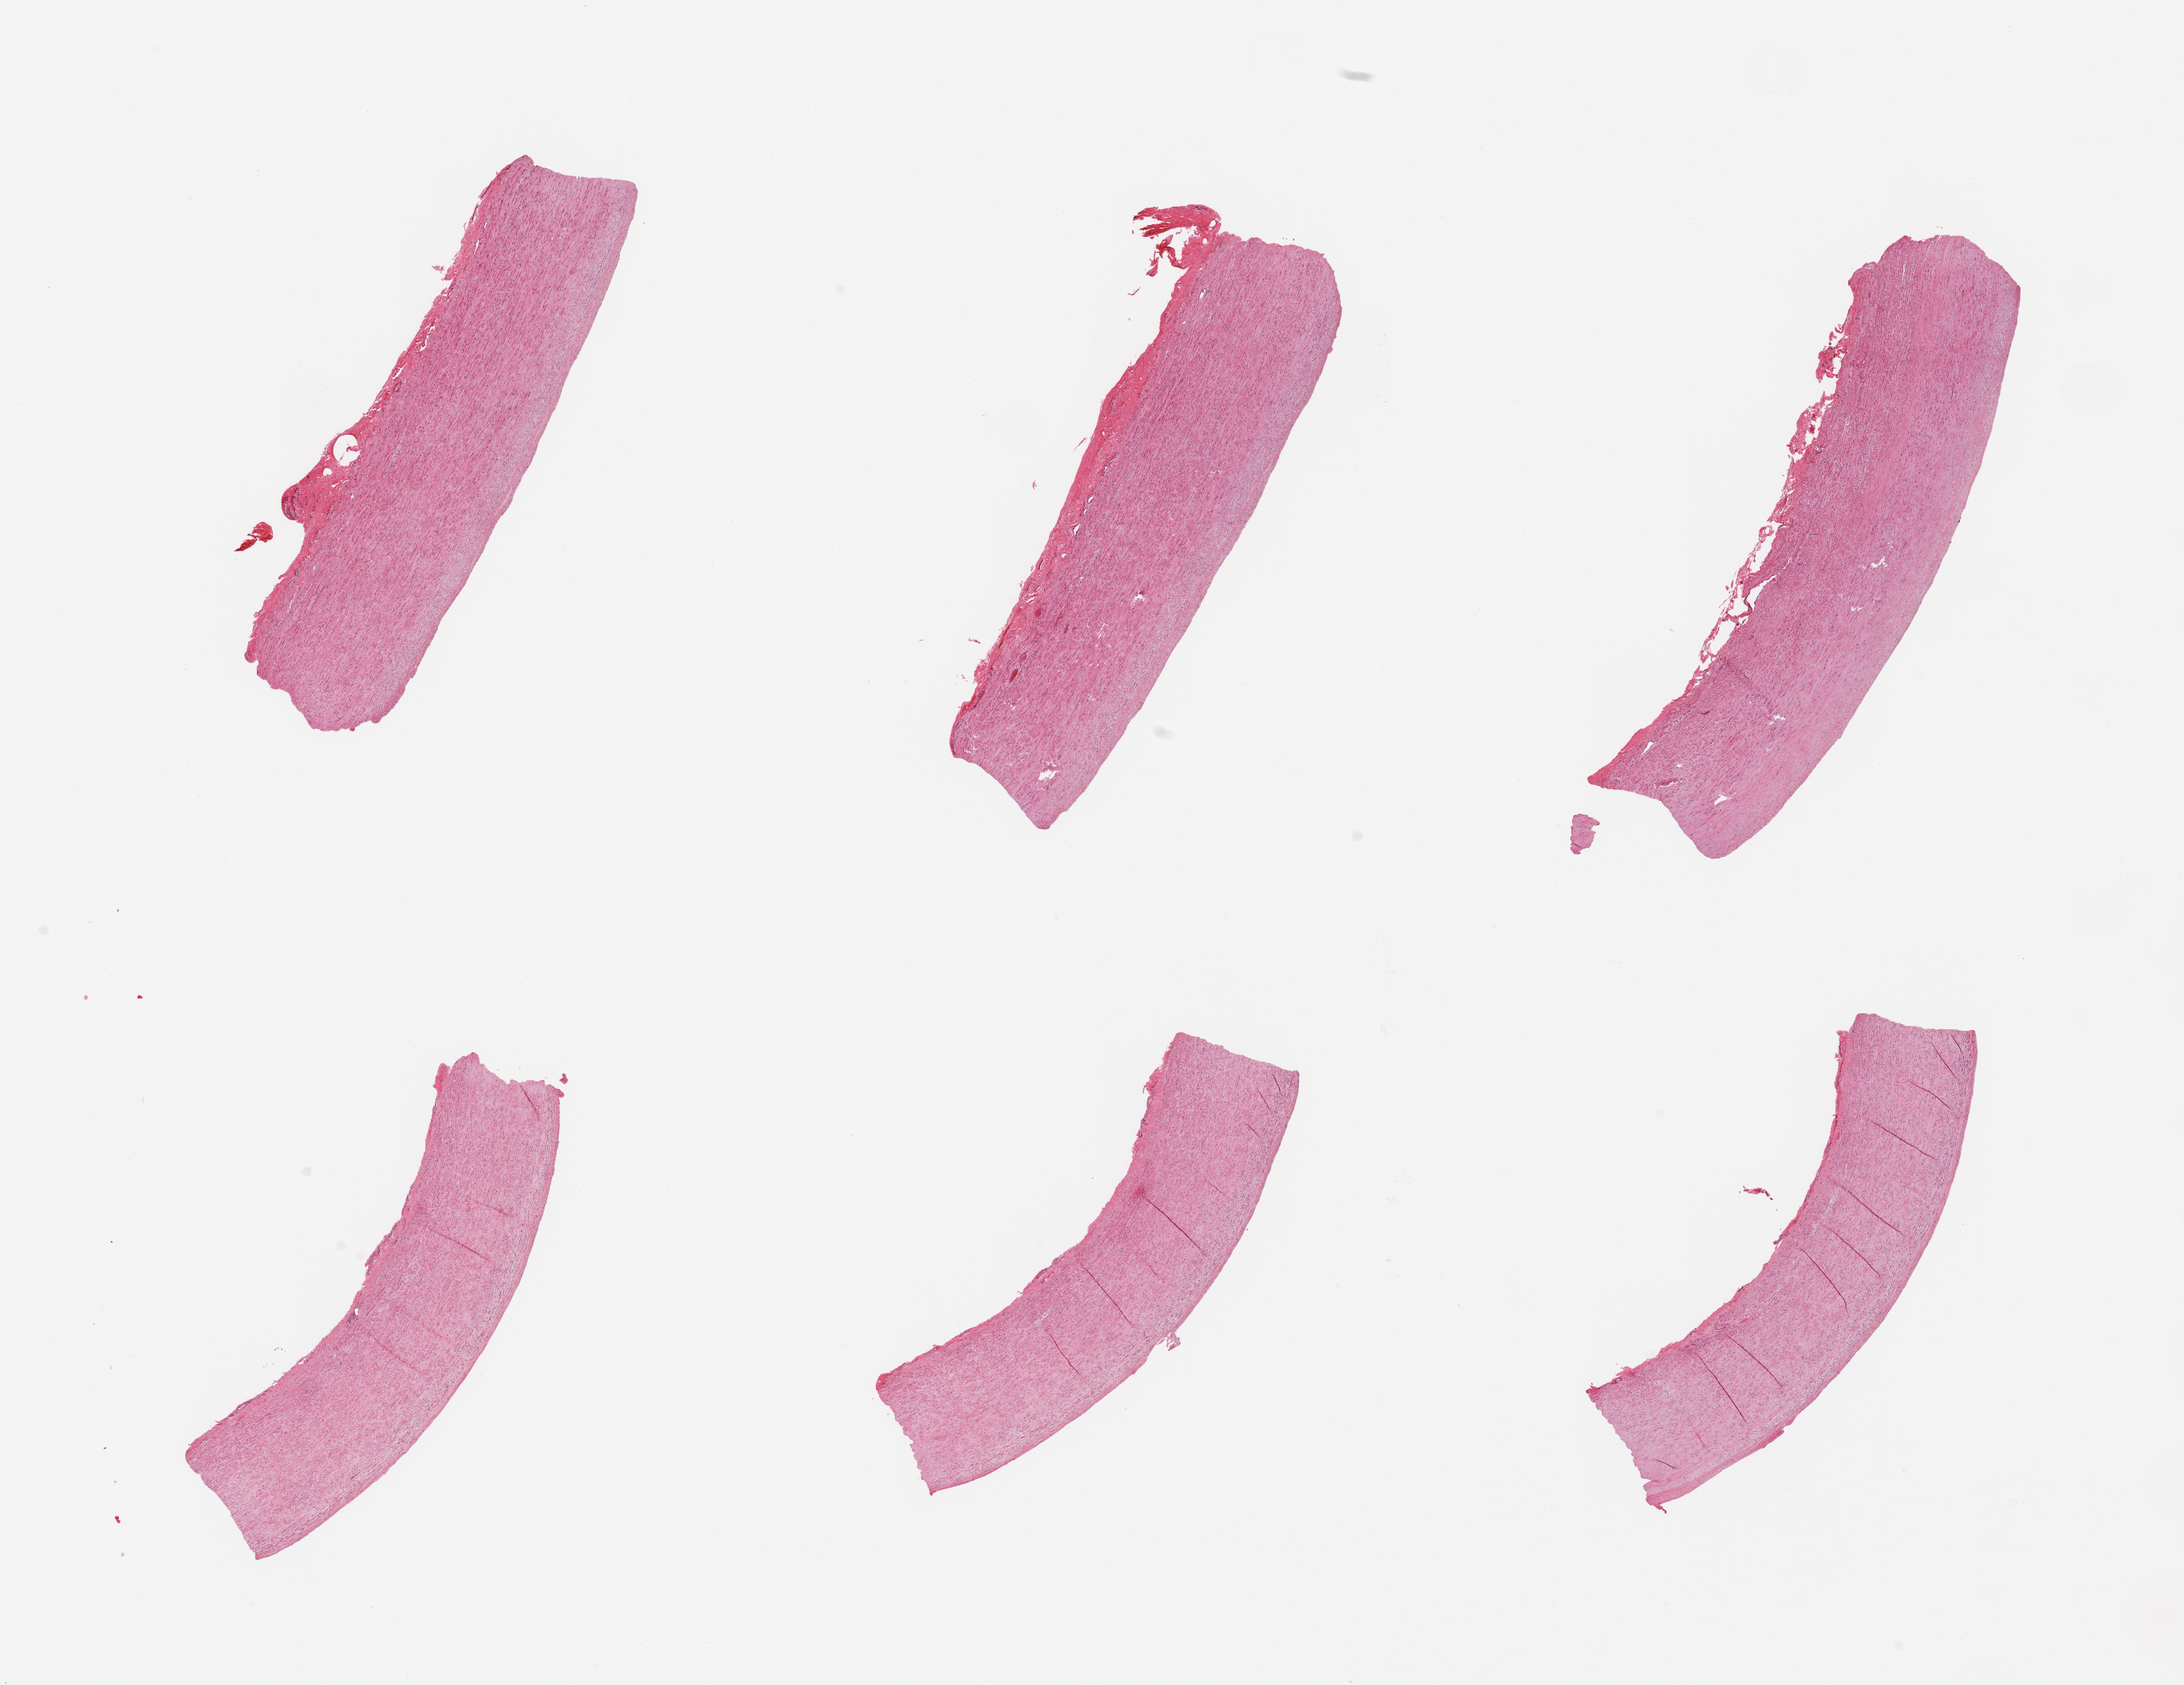
Digitized hematoxylin and eosin (H&E)-stained section — low-resolution overview of the scanned area, about 21.7 x 16.7 mm; PAXgene-fixed paraffin-embedded (PFPE) section; target tissue: aorta; tissue donor sample. Male donor.
Pathologist's review note for this sample: 6 pieces, no significant atherosis.